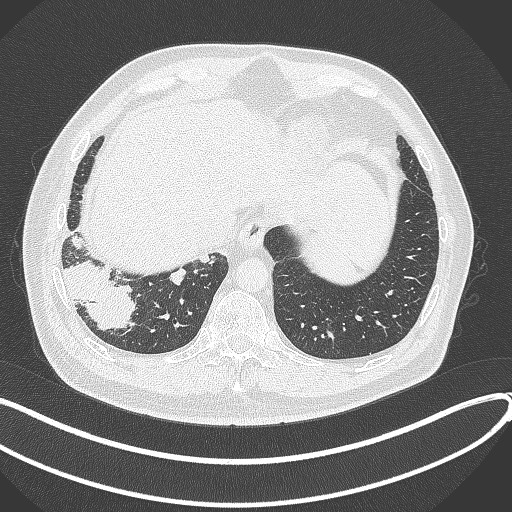
Chest CT, one axial slice. Slice 67 of 360 in the series (ordered by position). Reconstruction kernel B70f. 120 kVp. Lung window (W 1500 / L -600 HU). 1 mm slice thickness. 512 × 512 image matrix, field of view 400 × 400 mm. Patient: male, 59 years.
Annotated regions visible in this slice (bounding box drawn by a radiologist):
- lung tumour (recorded histology: adenocarcinoma): bounding box [x1, y1, x2, y2] px = [65, 253, 139, 334]